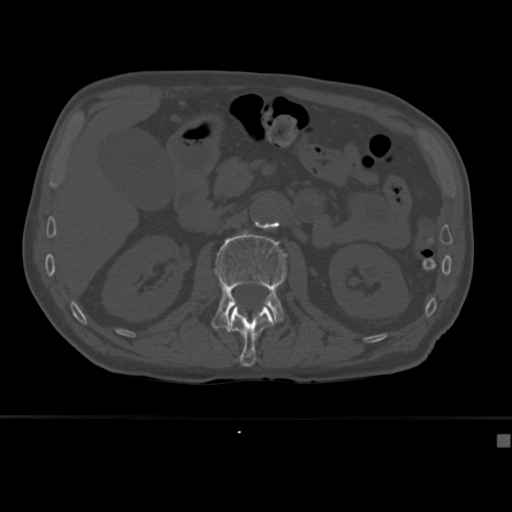
CT including the spine, one axial slice. Position 158 of 430 along the scan axis. 120 kVp. Bone window (W 1800 / L 400 HU). 512 × 512 image matrix, field of view 337 × 337 mm. Male patient, age 64 years. From the clinical record (not read from this slice): primary cancer: uterus; vertebrae with lytic lesions (as recorded): T1, T4, T5, T7, L5.
Outlined on this slice (semi-automatically segmented with operator editing):
- L1 vertebra: box from (x=229, y=307) to (x=274, y=367) px
- L2 vertebra: (x=212, y=231)–(x=288, y=334)